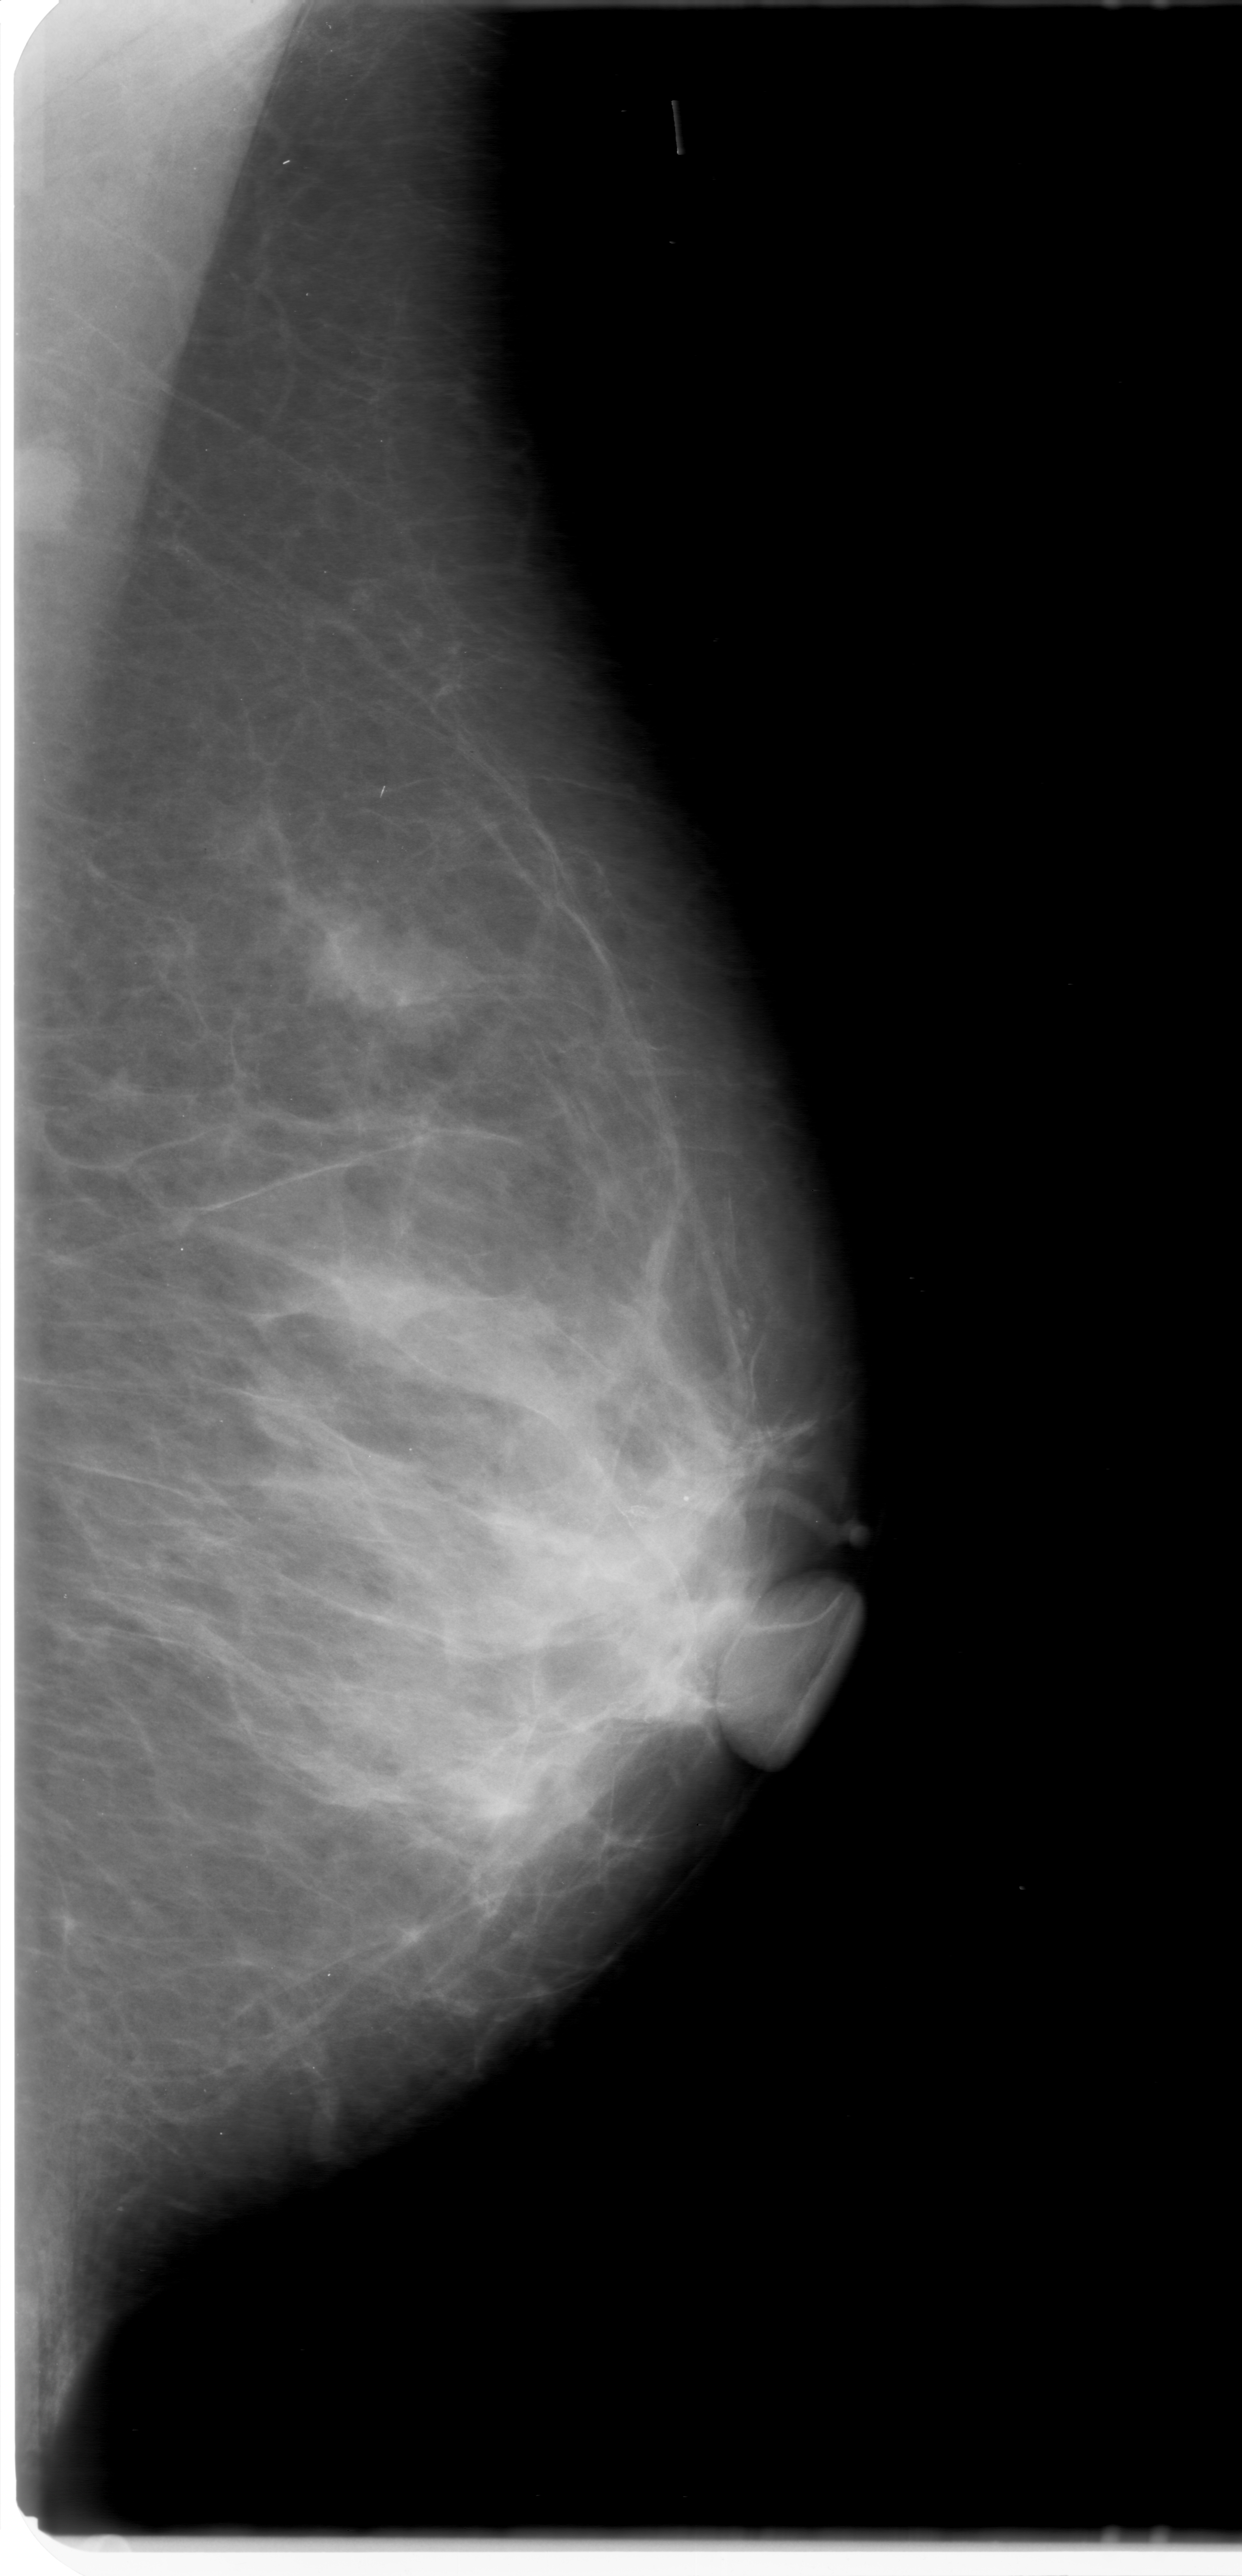
Digitized screen-film mammogram. Left breast. MLO view. Breast composition: scattered fibroglandular densities (BI-RADS density category 2 of 4). 1242 × 2576 image matrix.
Expert-marked regions of interest on this film, with their recorded descriptors:
- mass, shape lobulated, margins obscured; BI-RADS assessment category 0; subtlety rating 5 on a 1 (subtle) to 5 (obvious) scale; pathology result (as recorded, not read from the image): malignant: bounding box <297,897,477,1059> (left, top, right, bottom; pixels)